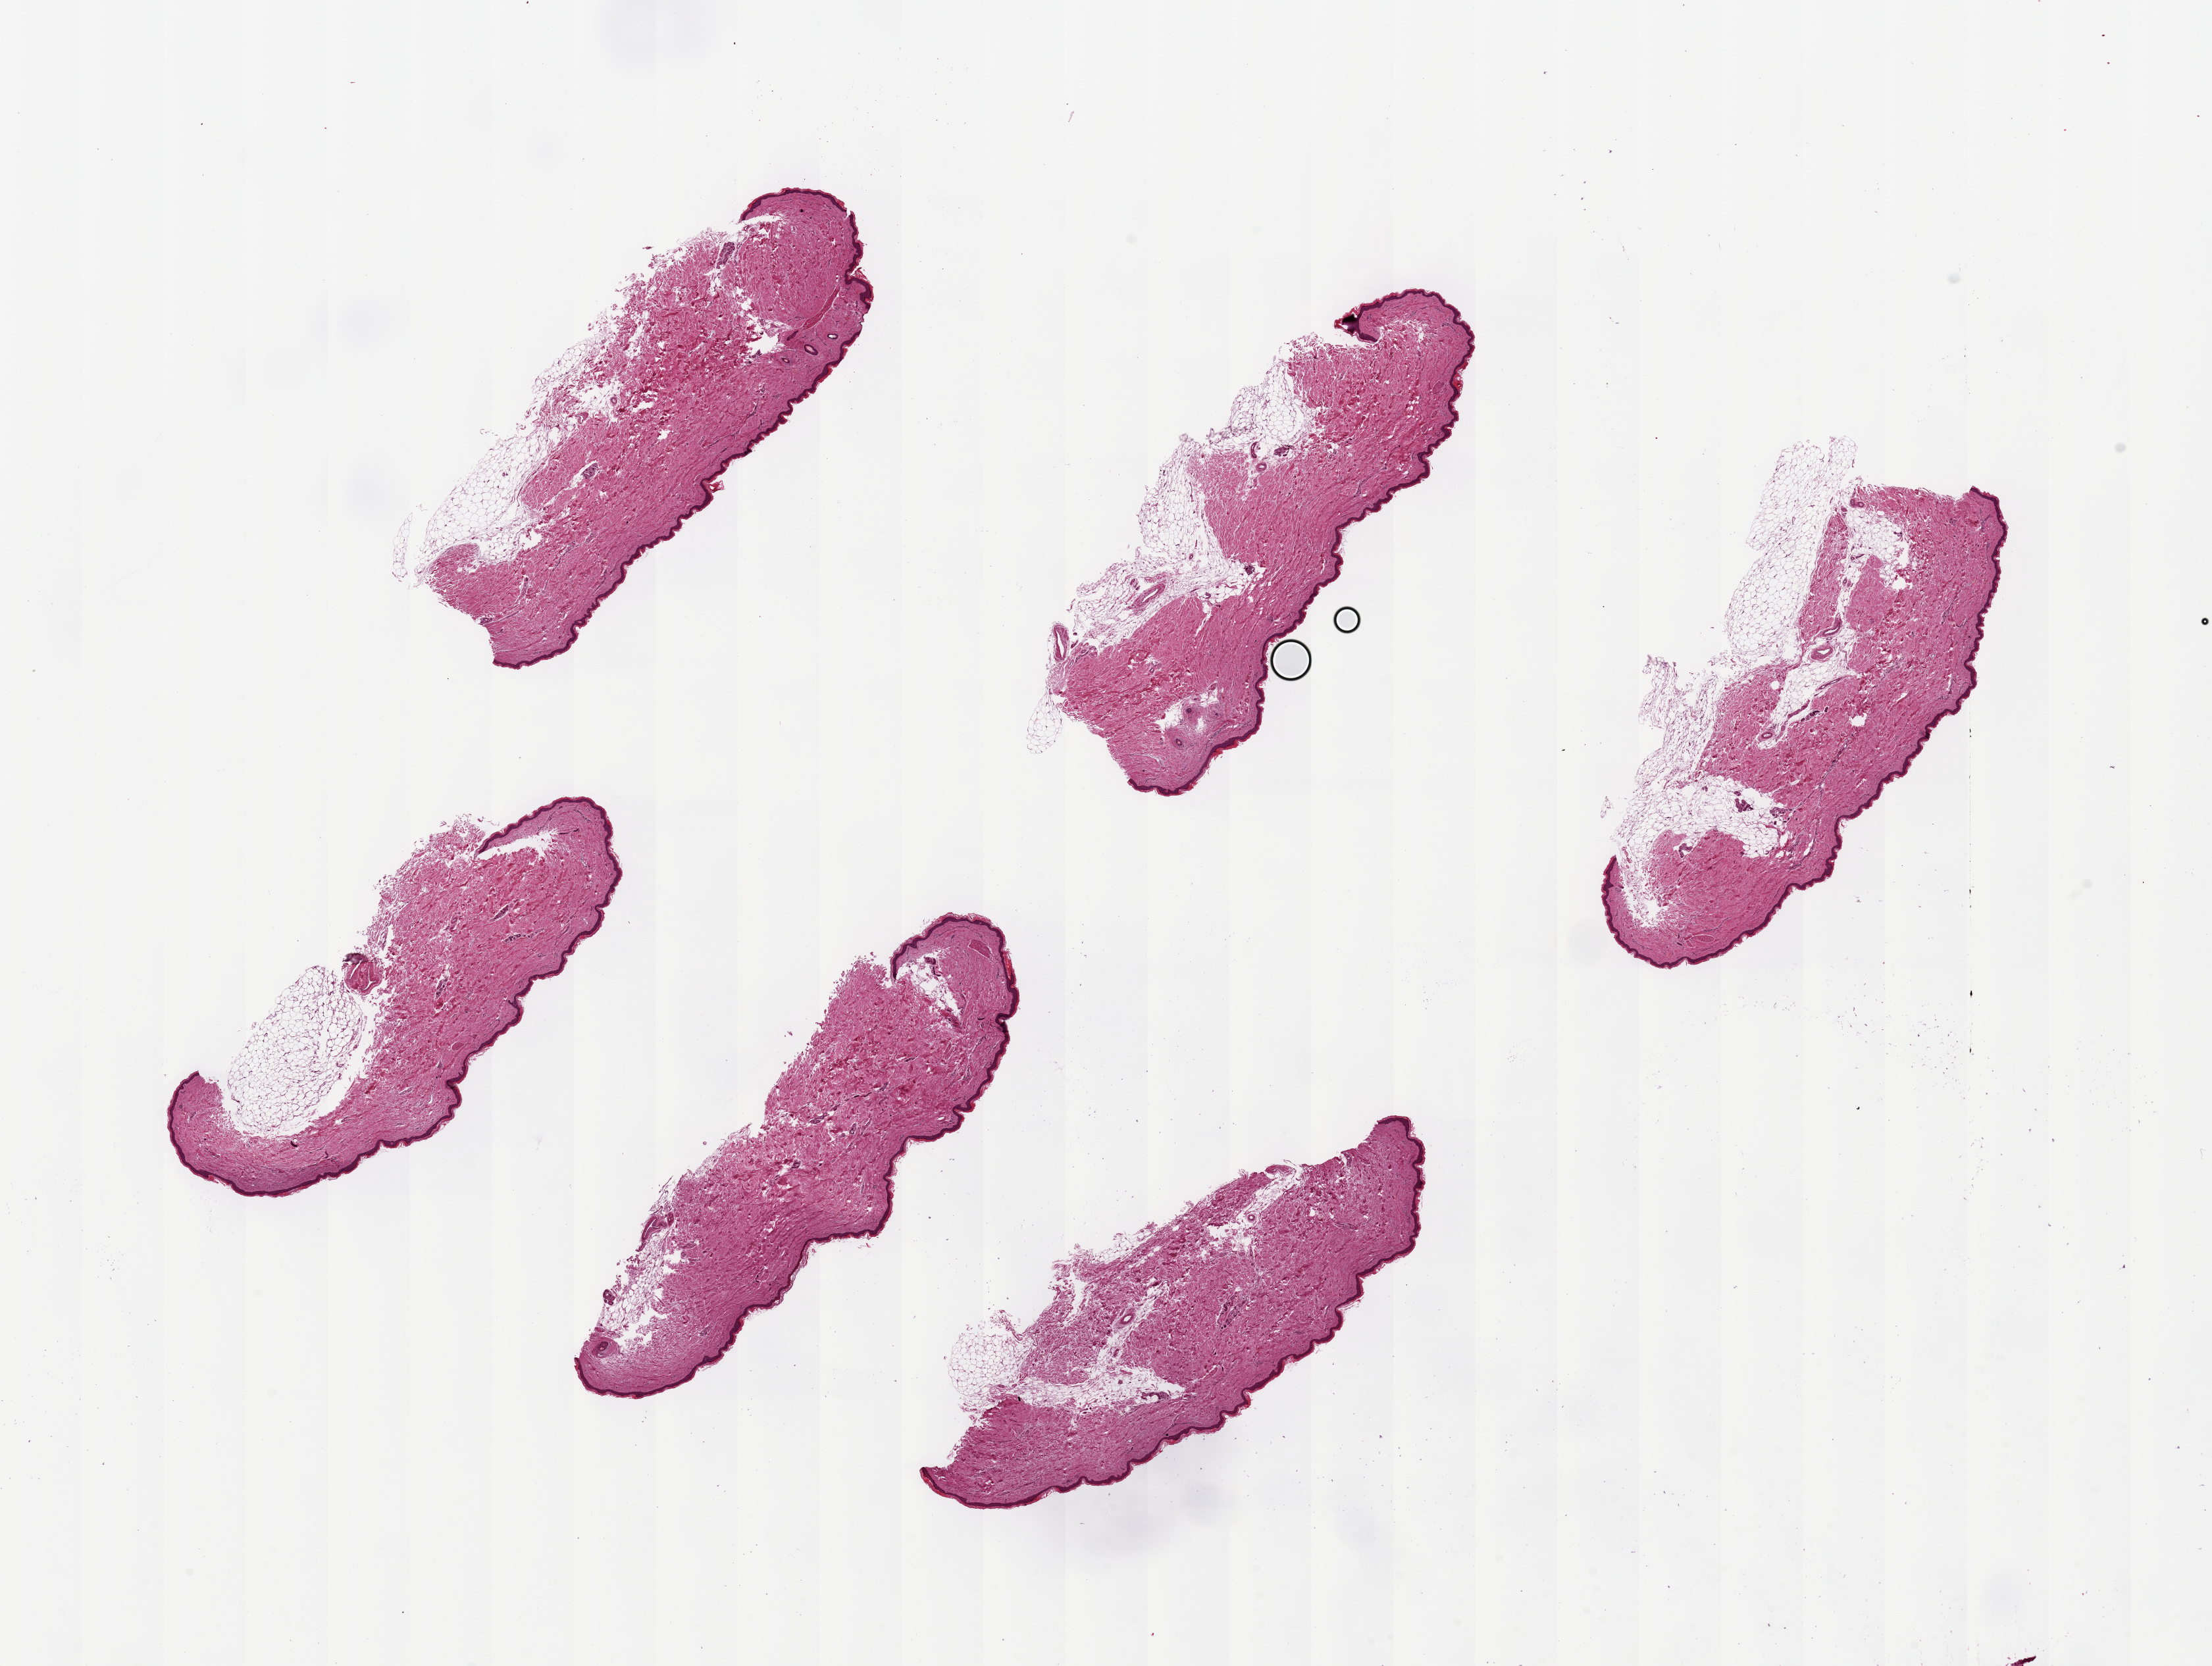
Digitized hematoxylin and eosin (H&E)-stained section, low-resolution overview of the scanned area, about 26.6 x 20.0 mm. PAXgene-fixed, paraffin-embedded tissue. Target tissue: skin of lower leg. Donor tissue sample. Female donor.
Pathologist's review note for this sample: 6 pieces ~7x2mm; squamous epithelium is ~1-2% of thickness.